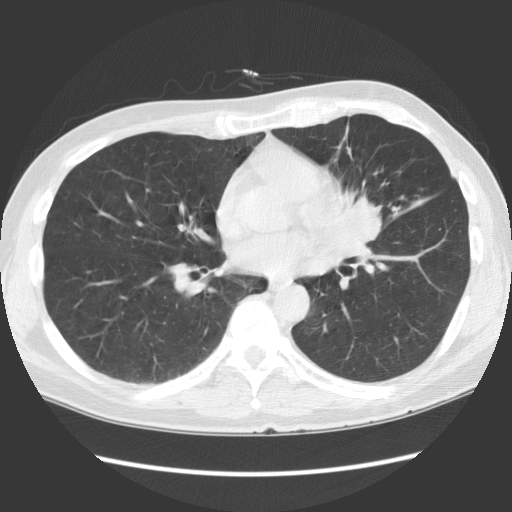
Low-dose screening chest CT, one axial slice. Slice 64 of 136 in the series (ordered by position). Reconstruction kernel STANDARD. 140 kVp. Lung window (W 1500 / L -600 HU). 2.5 mm slice thickness. 512 × 512 image matrix, field of view 360 × 360 mm.
Structures marked on this image (outlined manually by an expert reader):
- lesion 1 (tumor, hilum of left lung): bounding box [x1, y1, x2, y2] px = [337, 190, 382, 240]